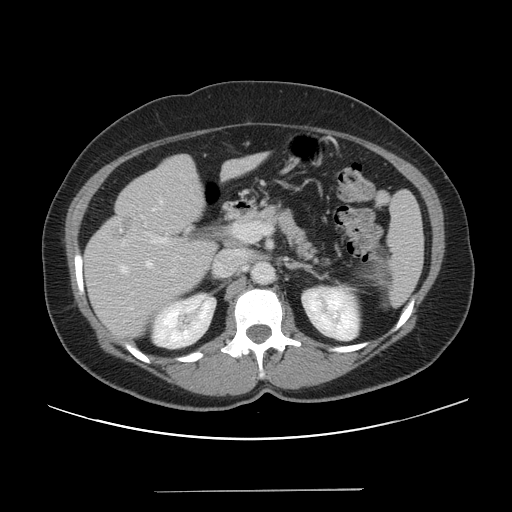
Contrast-enhanced abdominal CT, one axial slice. Slice 24 of 56 in the series (ordered by position). 120 kVp. Intravenous contrast given. Soft-tissue window (W 400 / L 40 HU). 5 mm slice thickness. 512 × 512 image matrix, field of view 419 × 419 mm. Female patient, age 54 years. Case-level facts recorded for this patient, not image findings: diagnosis: colorectal cancer liver metastases, imaged before liver resection.
Annotated regions visible in this slice (expert manual segmentation):
- hepatic veins: bounding box (x1, y1, x2, y2) in pixels: (121, 261, 152, 310)
- liver: (84, 154, 265, 339)
- planned liver remnant (the part of the liver to remain after resection): (164, 154, 265, 207)
- portal vein (with intrahepatic branches): (151, 223, 270, 243)
- liver metastasis: (119, 216, 133, 236)